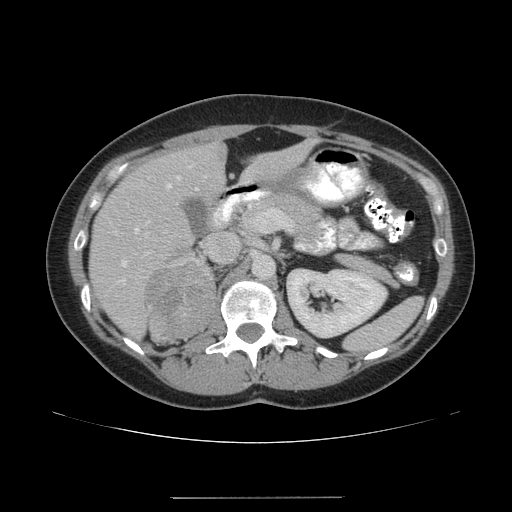
Contrast-enhanced abdominal CT, one axial slice; position 106 of 161 along the scan axis; reconstruction kernel STANDARD; 120 kVp; intravenous contrast given; soft-tissue window (W 400 / L 40 HU); 3.75 mm slice thickness; 512 × 512 image matrix, field of view 380 × 380 mm. Female patient. Case-level facts recorded for this patient, not image findings: diagnosis: adrenocortical carcinoma; tumour side: right adrenal; tumour size at pathology: 9 cm; Ki-67 index: 14 %; stage (as recorded): 3.
Outlined on this slice (semi-automatic segmentation, software-assisted and operator-edited):
- mass: bounding box [x1, y1, x2, y2] px = [147, 262, 214, 344]